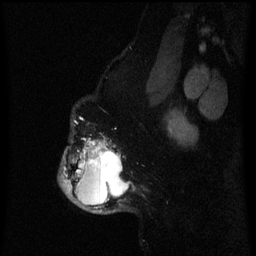
Breast MRI (dynamic contrast-enhanced), one sagittal slice. Position 51 of 60 along the scan axis. Dynamic contrast-enhanced series, image 2 of 3 at this slice position (ordered by acquisition). 1.5 T. TE 4.2 ms, TR 8 ms. 256 × 256 image matrix, field of view 190 × 190 mm. Female patient, age 50 years.
Outlined on this slice (semi-automatically segmented with operator editing):
- analysis volume of interest (the breast-tissue region the enhancement analysis was run in; not a lesion): bounding box <58,136,135,214> (left, top, right, bottom; pixels)
- tumour enhancement mask (voxels above the 70 % enhancement threshold inside the analysis volume of interest): <62,140,122,208>